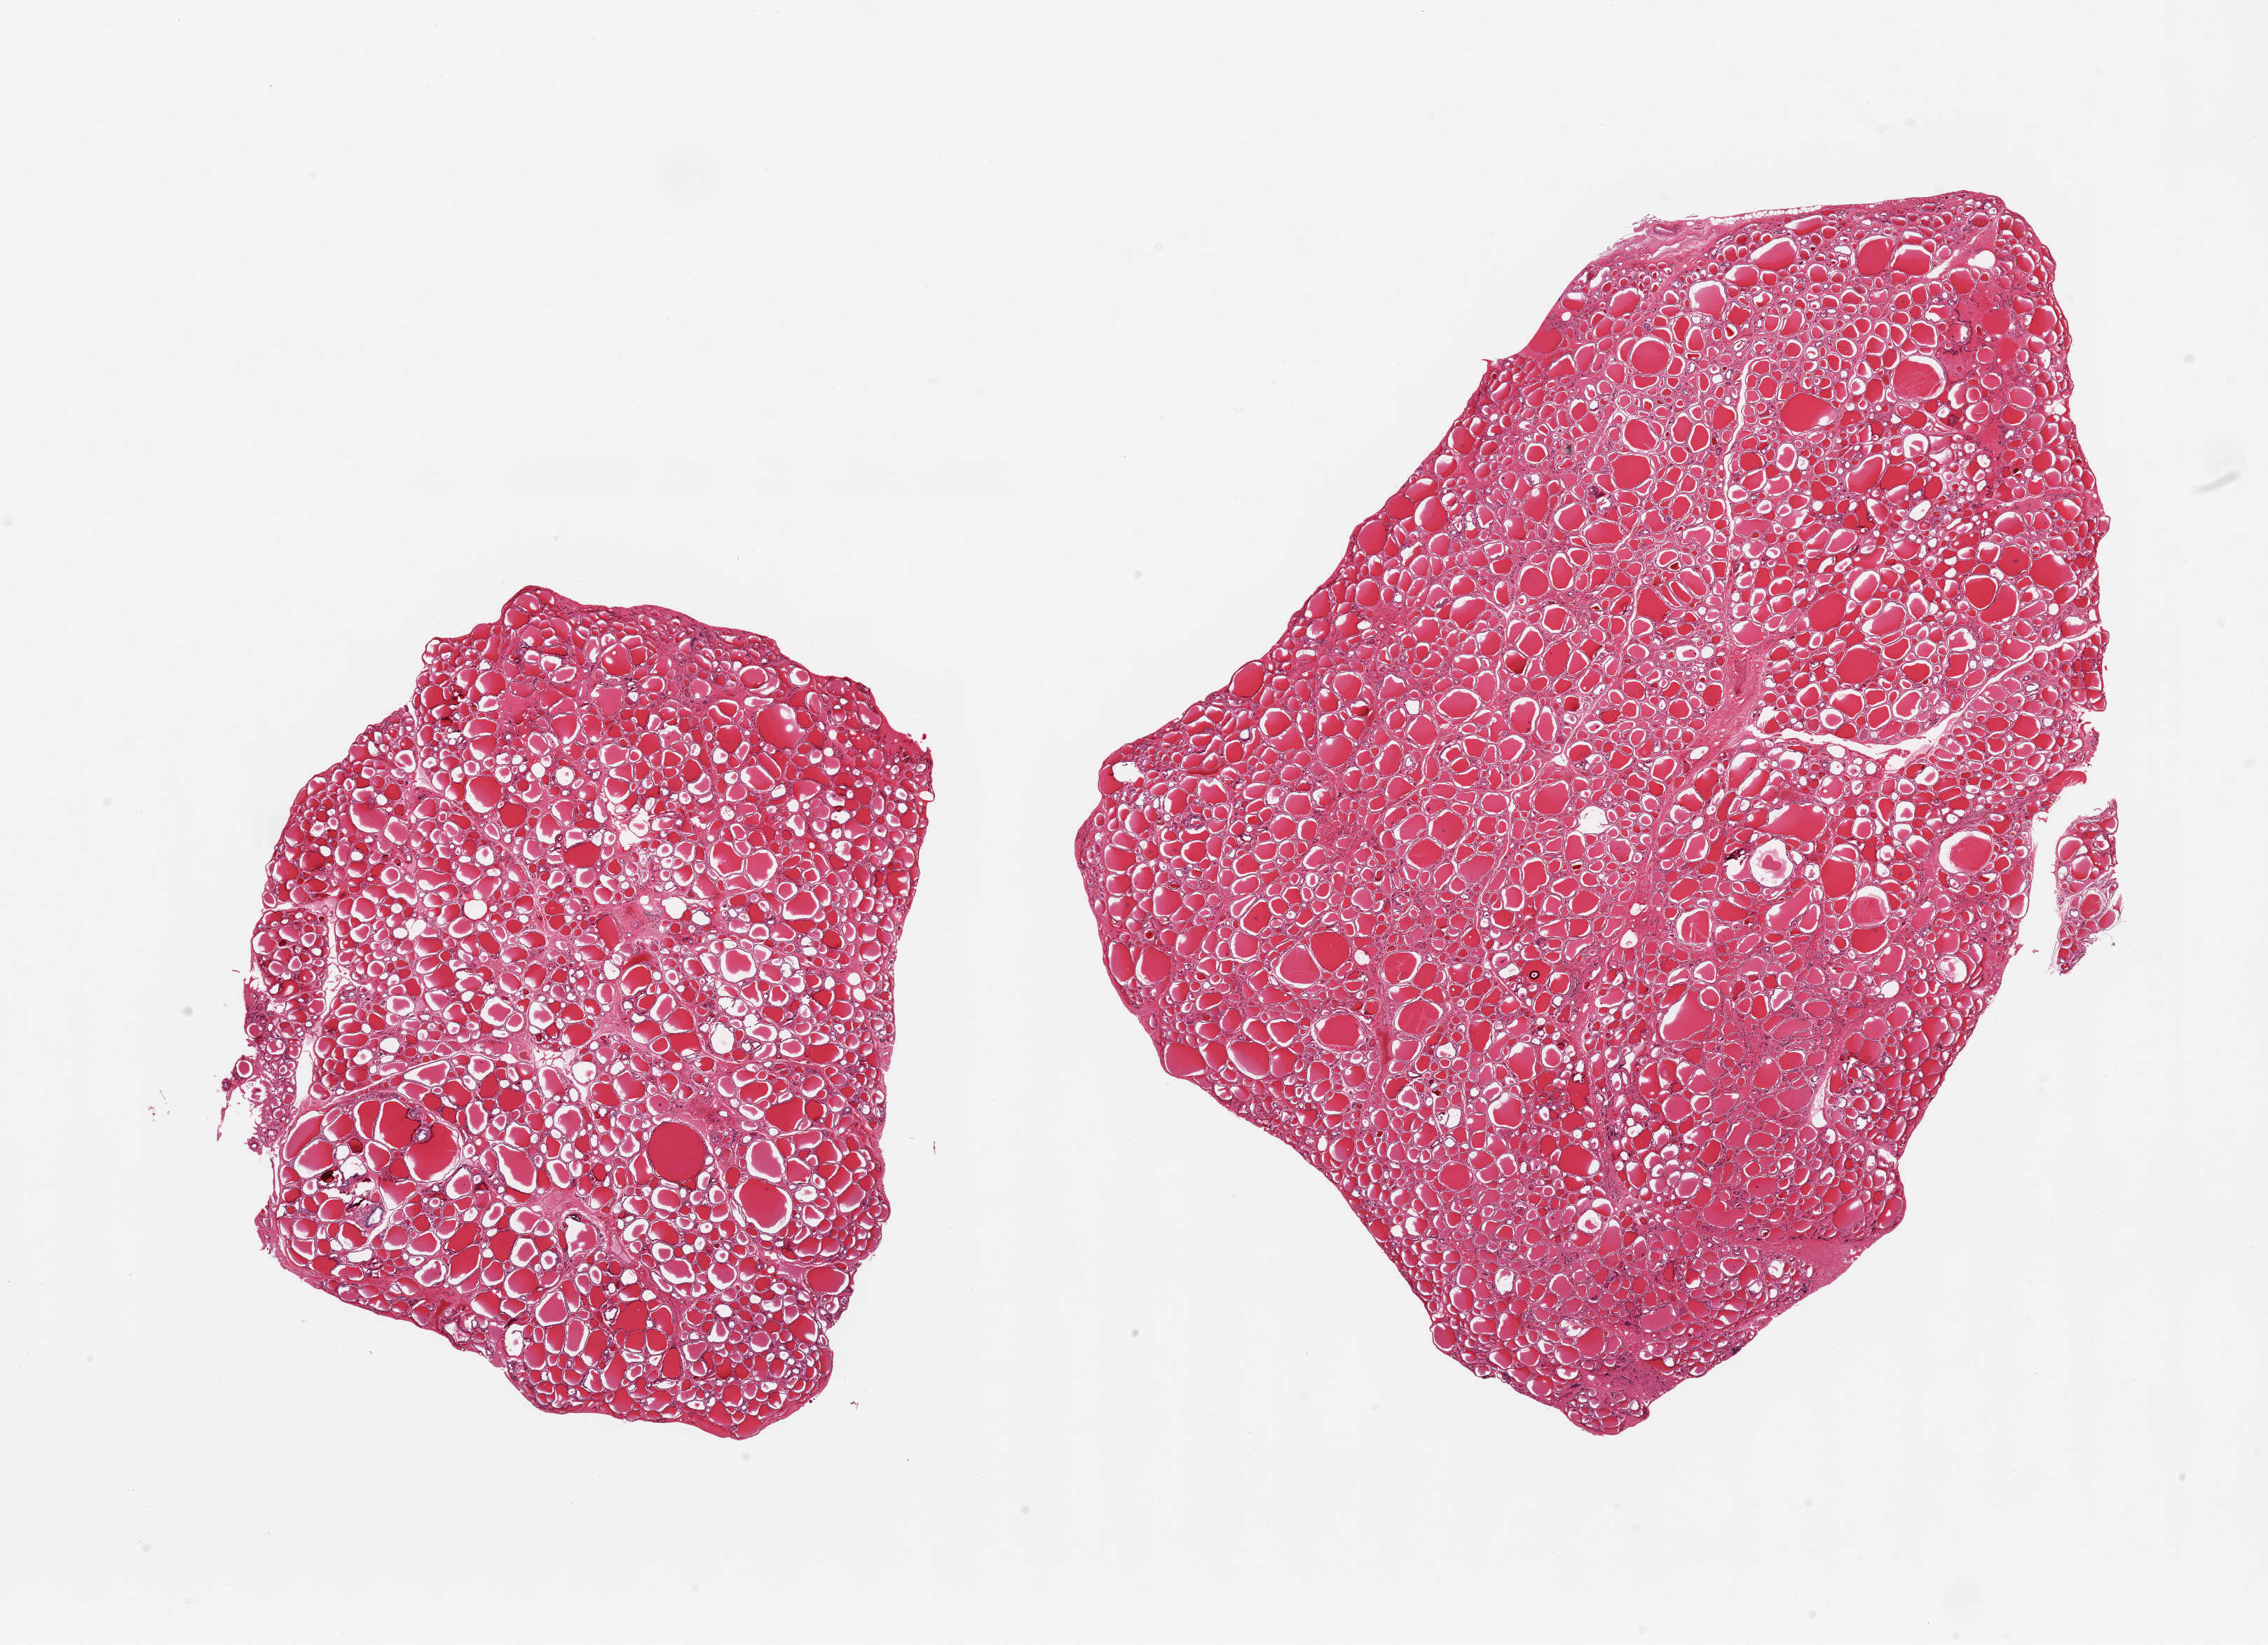
Haematoxylin and eosin whole-slide image, whole scanned area (about 25.6 x 18.6 mm, slide scanned at 20x) shown as a low-resolution overview. PAXgene-fixed, paraffin-embedded tissue. Section of thyroid (target tissue). Donor tissue sample.
Pathologist's review note for this sample: 2 pieces, no abnormalities.